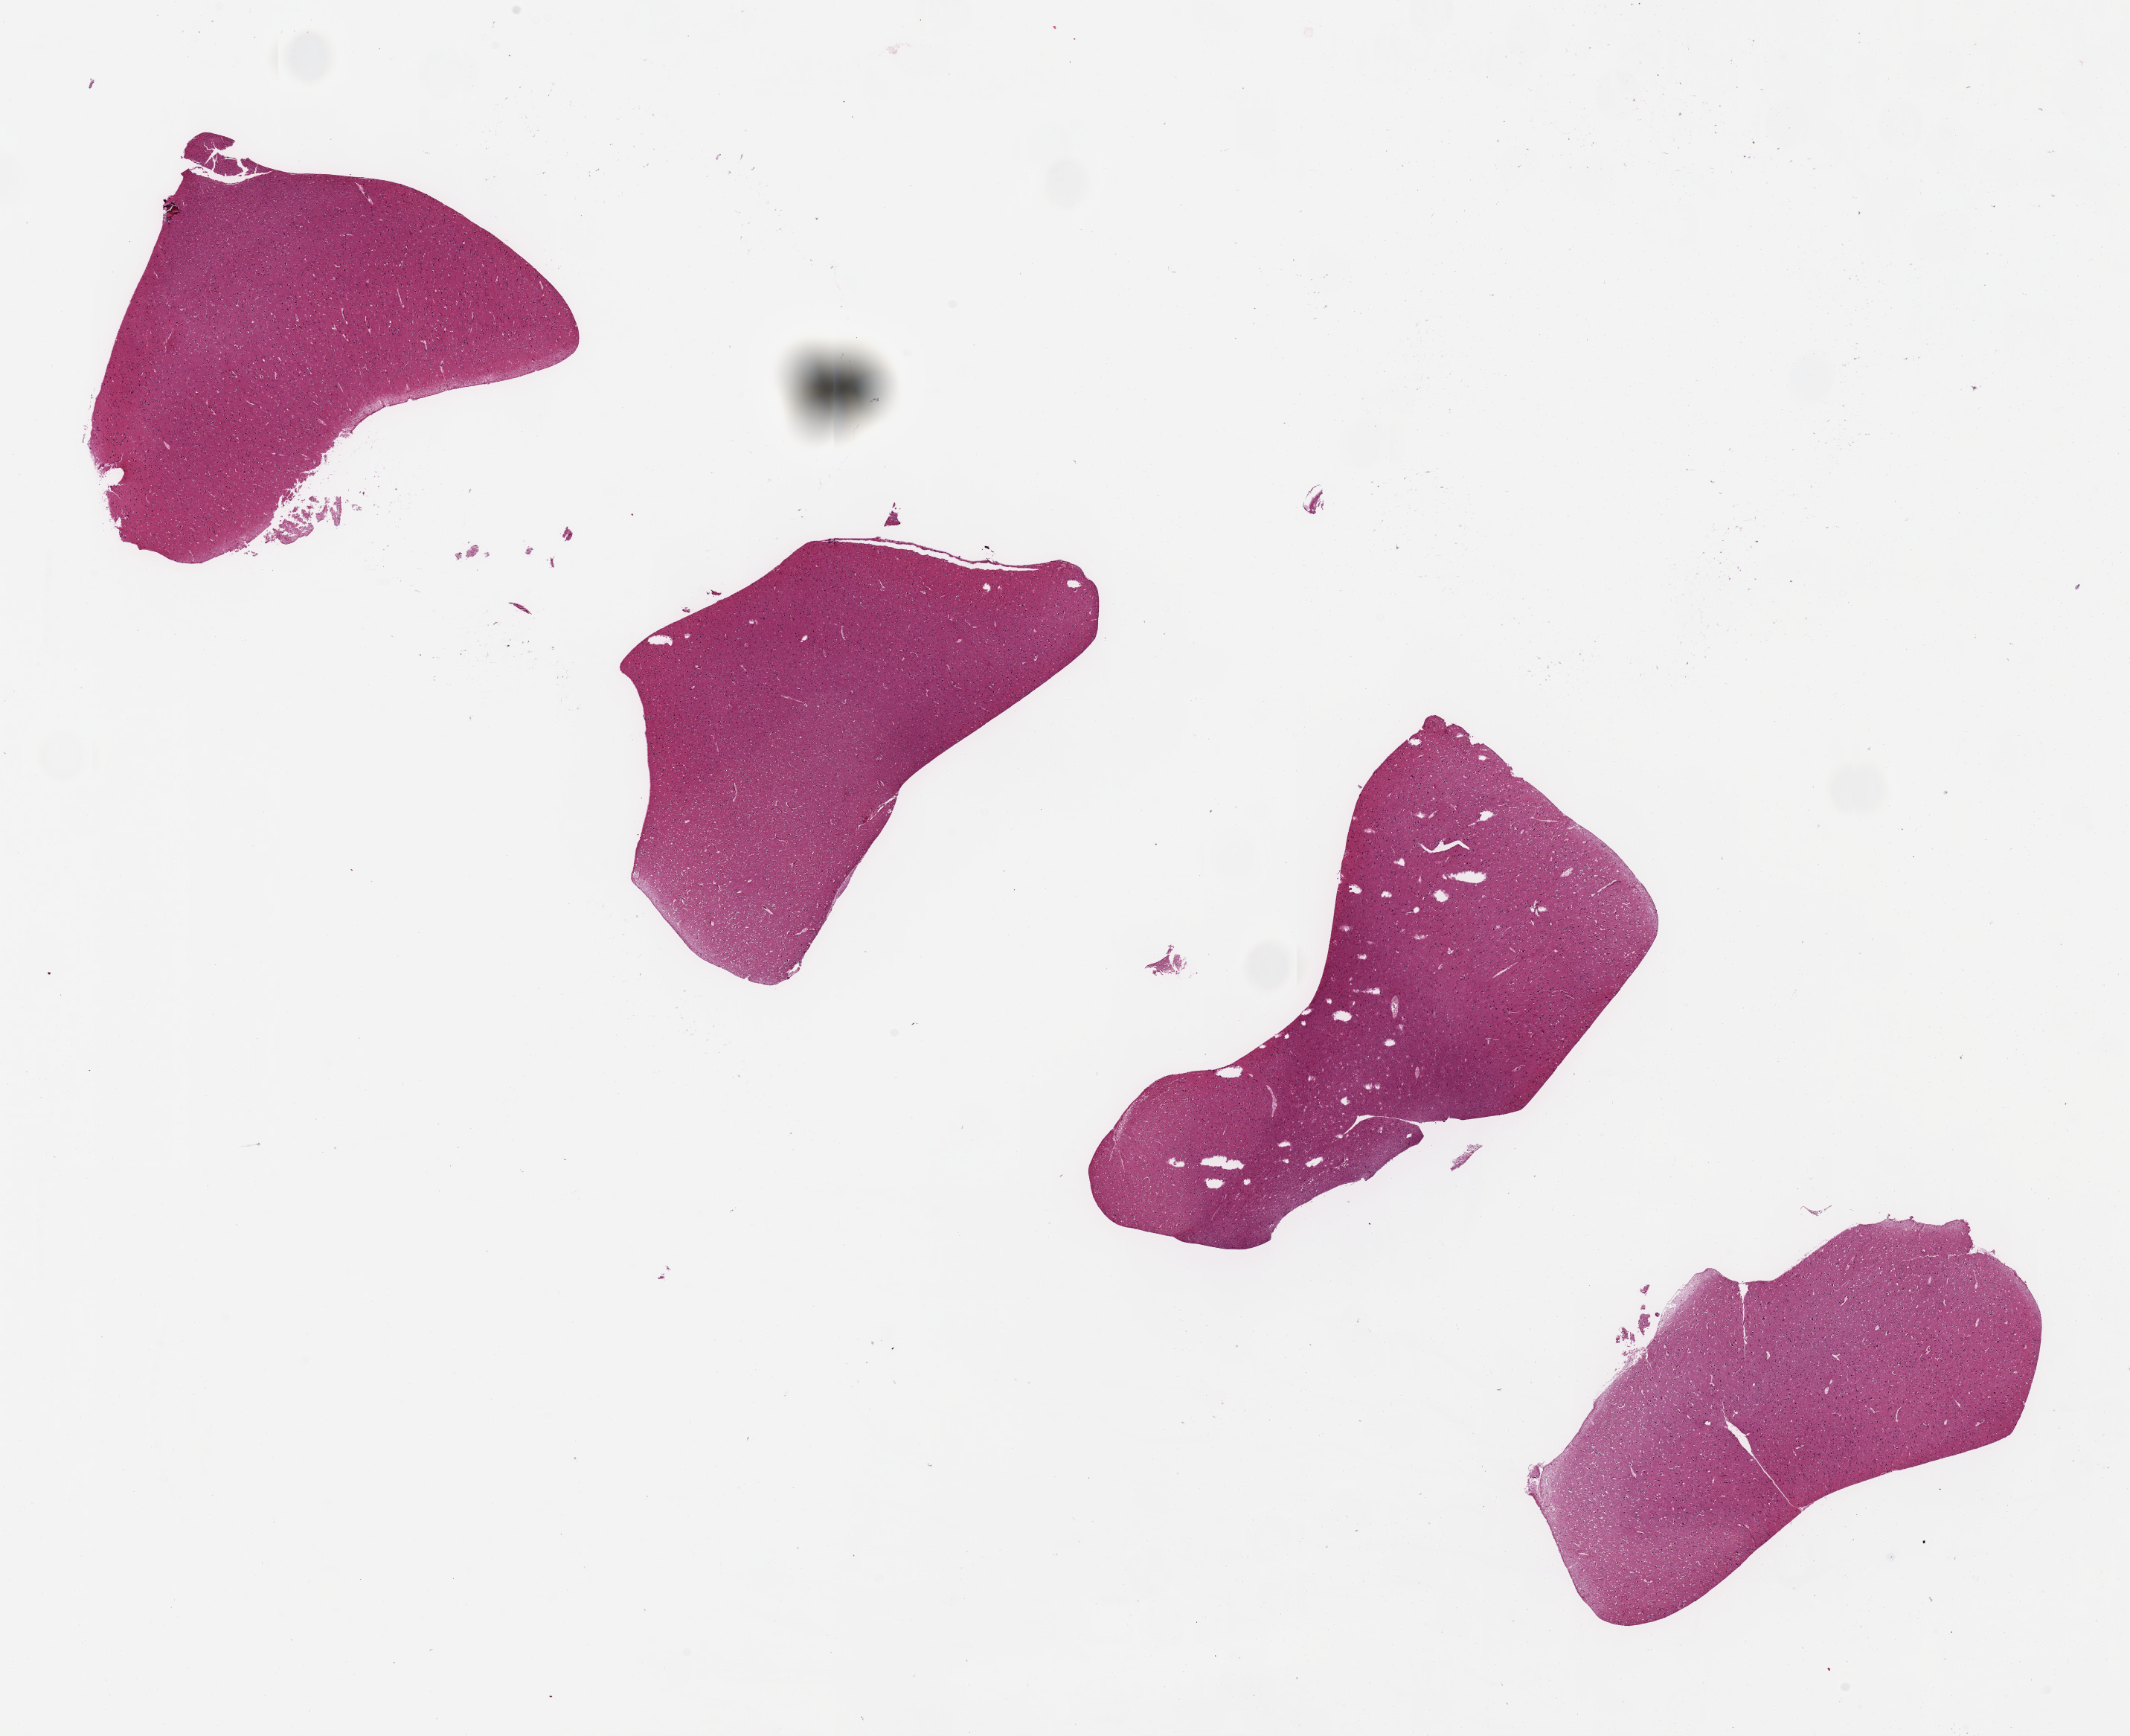
Whole-slide image, hematoxylin and eosin (H&E) stain — low-resolution overview of the scanned area, about 22.6 x 18.5 mm (acquisition: 20x scan). PAXgene-fixed paraffin-embedded (PFPE) section. Section of cerebral cortex (target tissue). Donor tissue sample. Donor sex: male.
• pathologist's review note for this sample: 4 pieces,~5-6x3mm; tissue tears